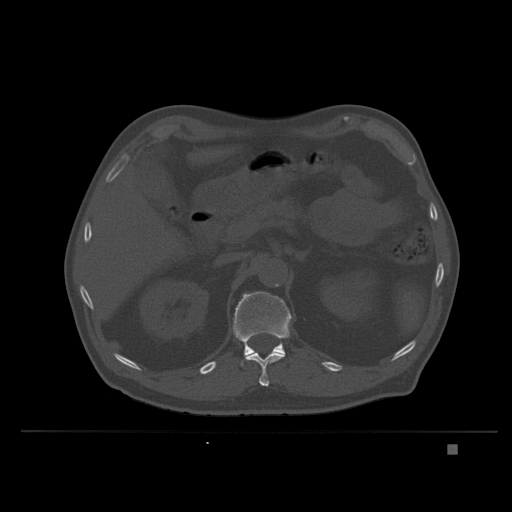
CT including the spine, one axial slice; position 148 of 435 along the scan axis; bone window (W 1800 / L 400 HU); 512 × 512 image matrix, field of view 434 × 434 mm. Male patient, age 73 years. Case-level facts recorded for this patient, not image findings: primary cancer: skin.
Annotated regions visible in this slice (semi-automatic segmentation, software-assisted and operator-edited):
- L1 vertebra: box from (x=233, y=291) to (x=292, y=366) px
- T12 vertebra: (x=246, y=351)–(x=285, y=387)